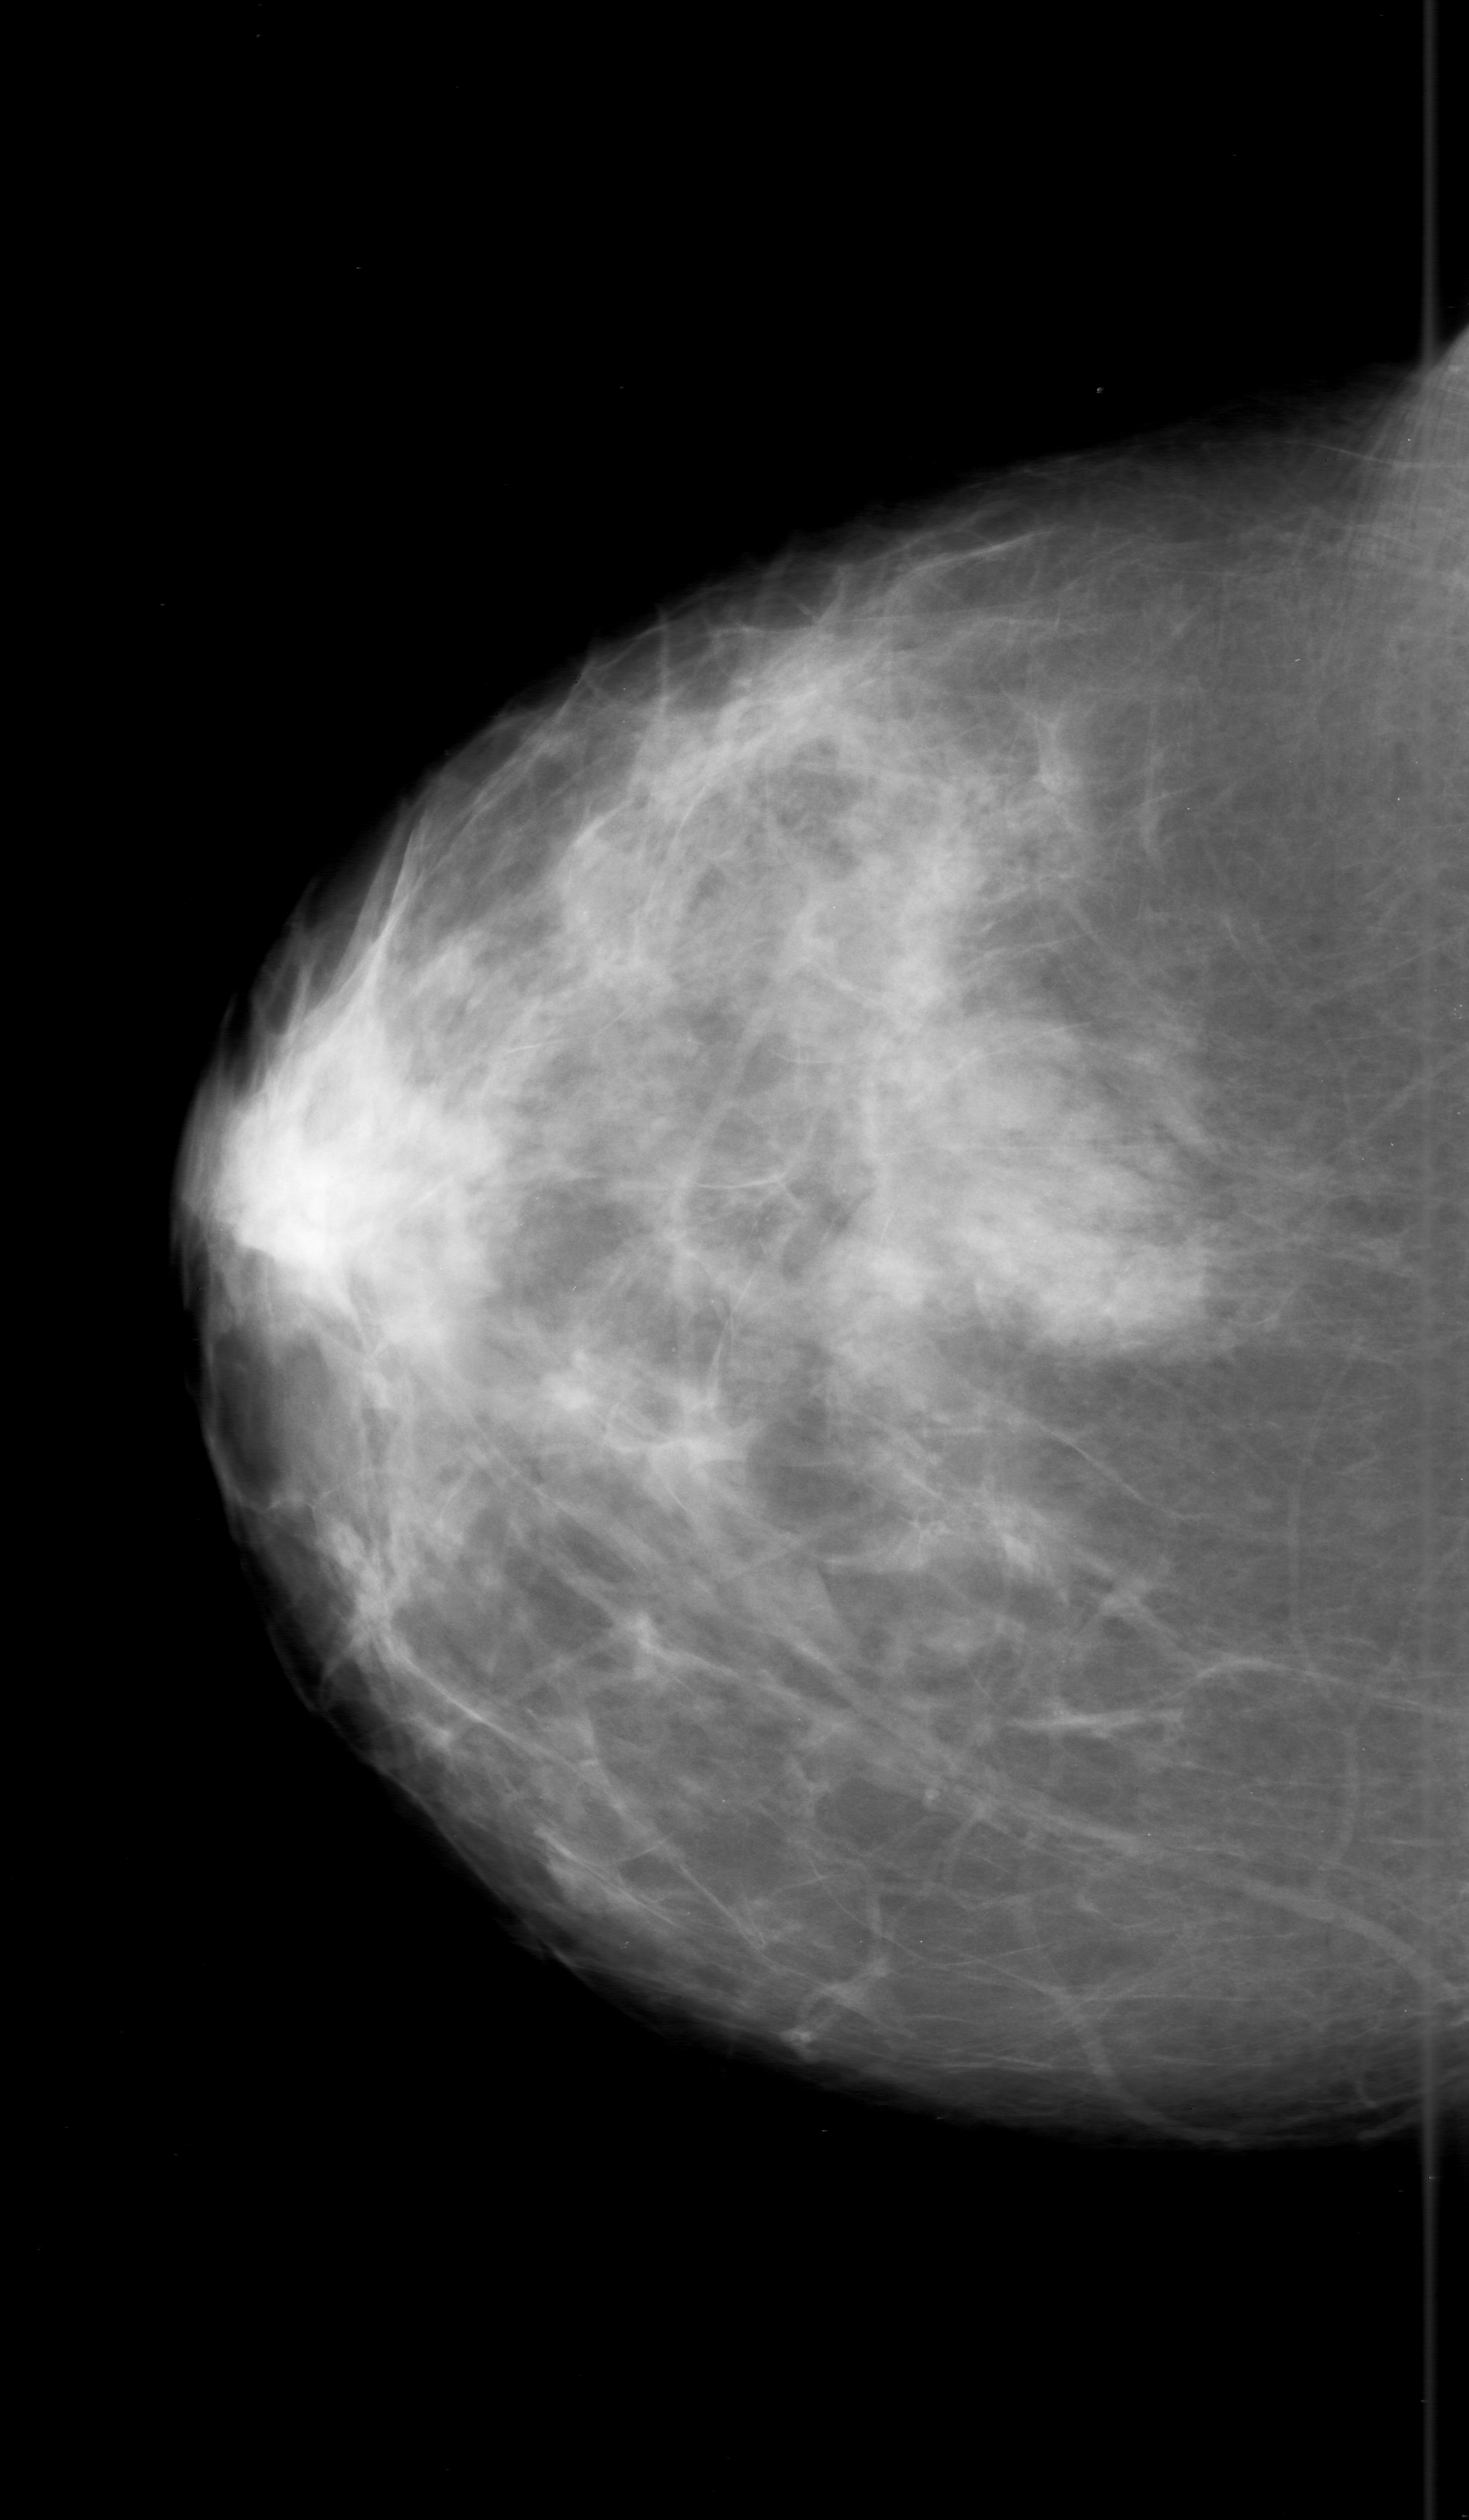
Digitized screen-film mammogram, right breast, craniocaudal (CC) view, breast composition: scattered fibroglandular densities (BI-RADS density category 2 of 4).
- Finding: calcifications, morphology punctate, distribution clustered; BI-RADS assessment category 0 (incomplete: needs additional imaging); subtlety rating 2 on a 1 (subtle) to 5 (obvious) scale; pathology (as recorded): benign.